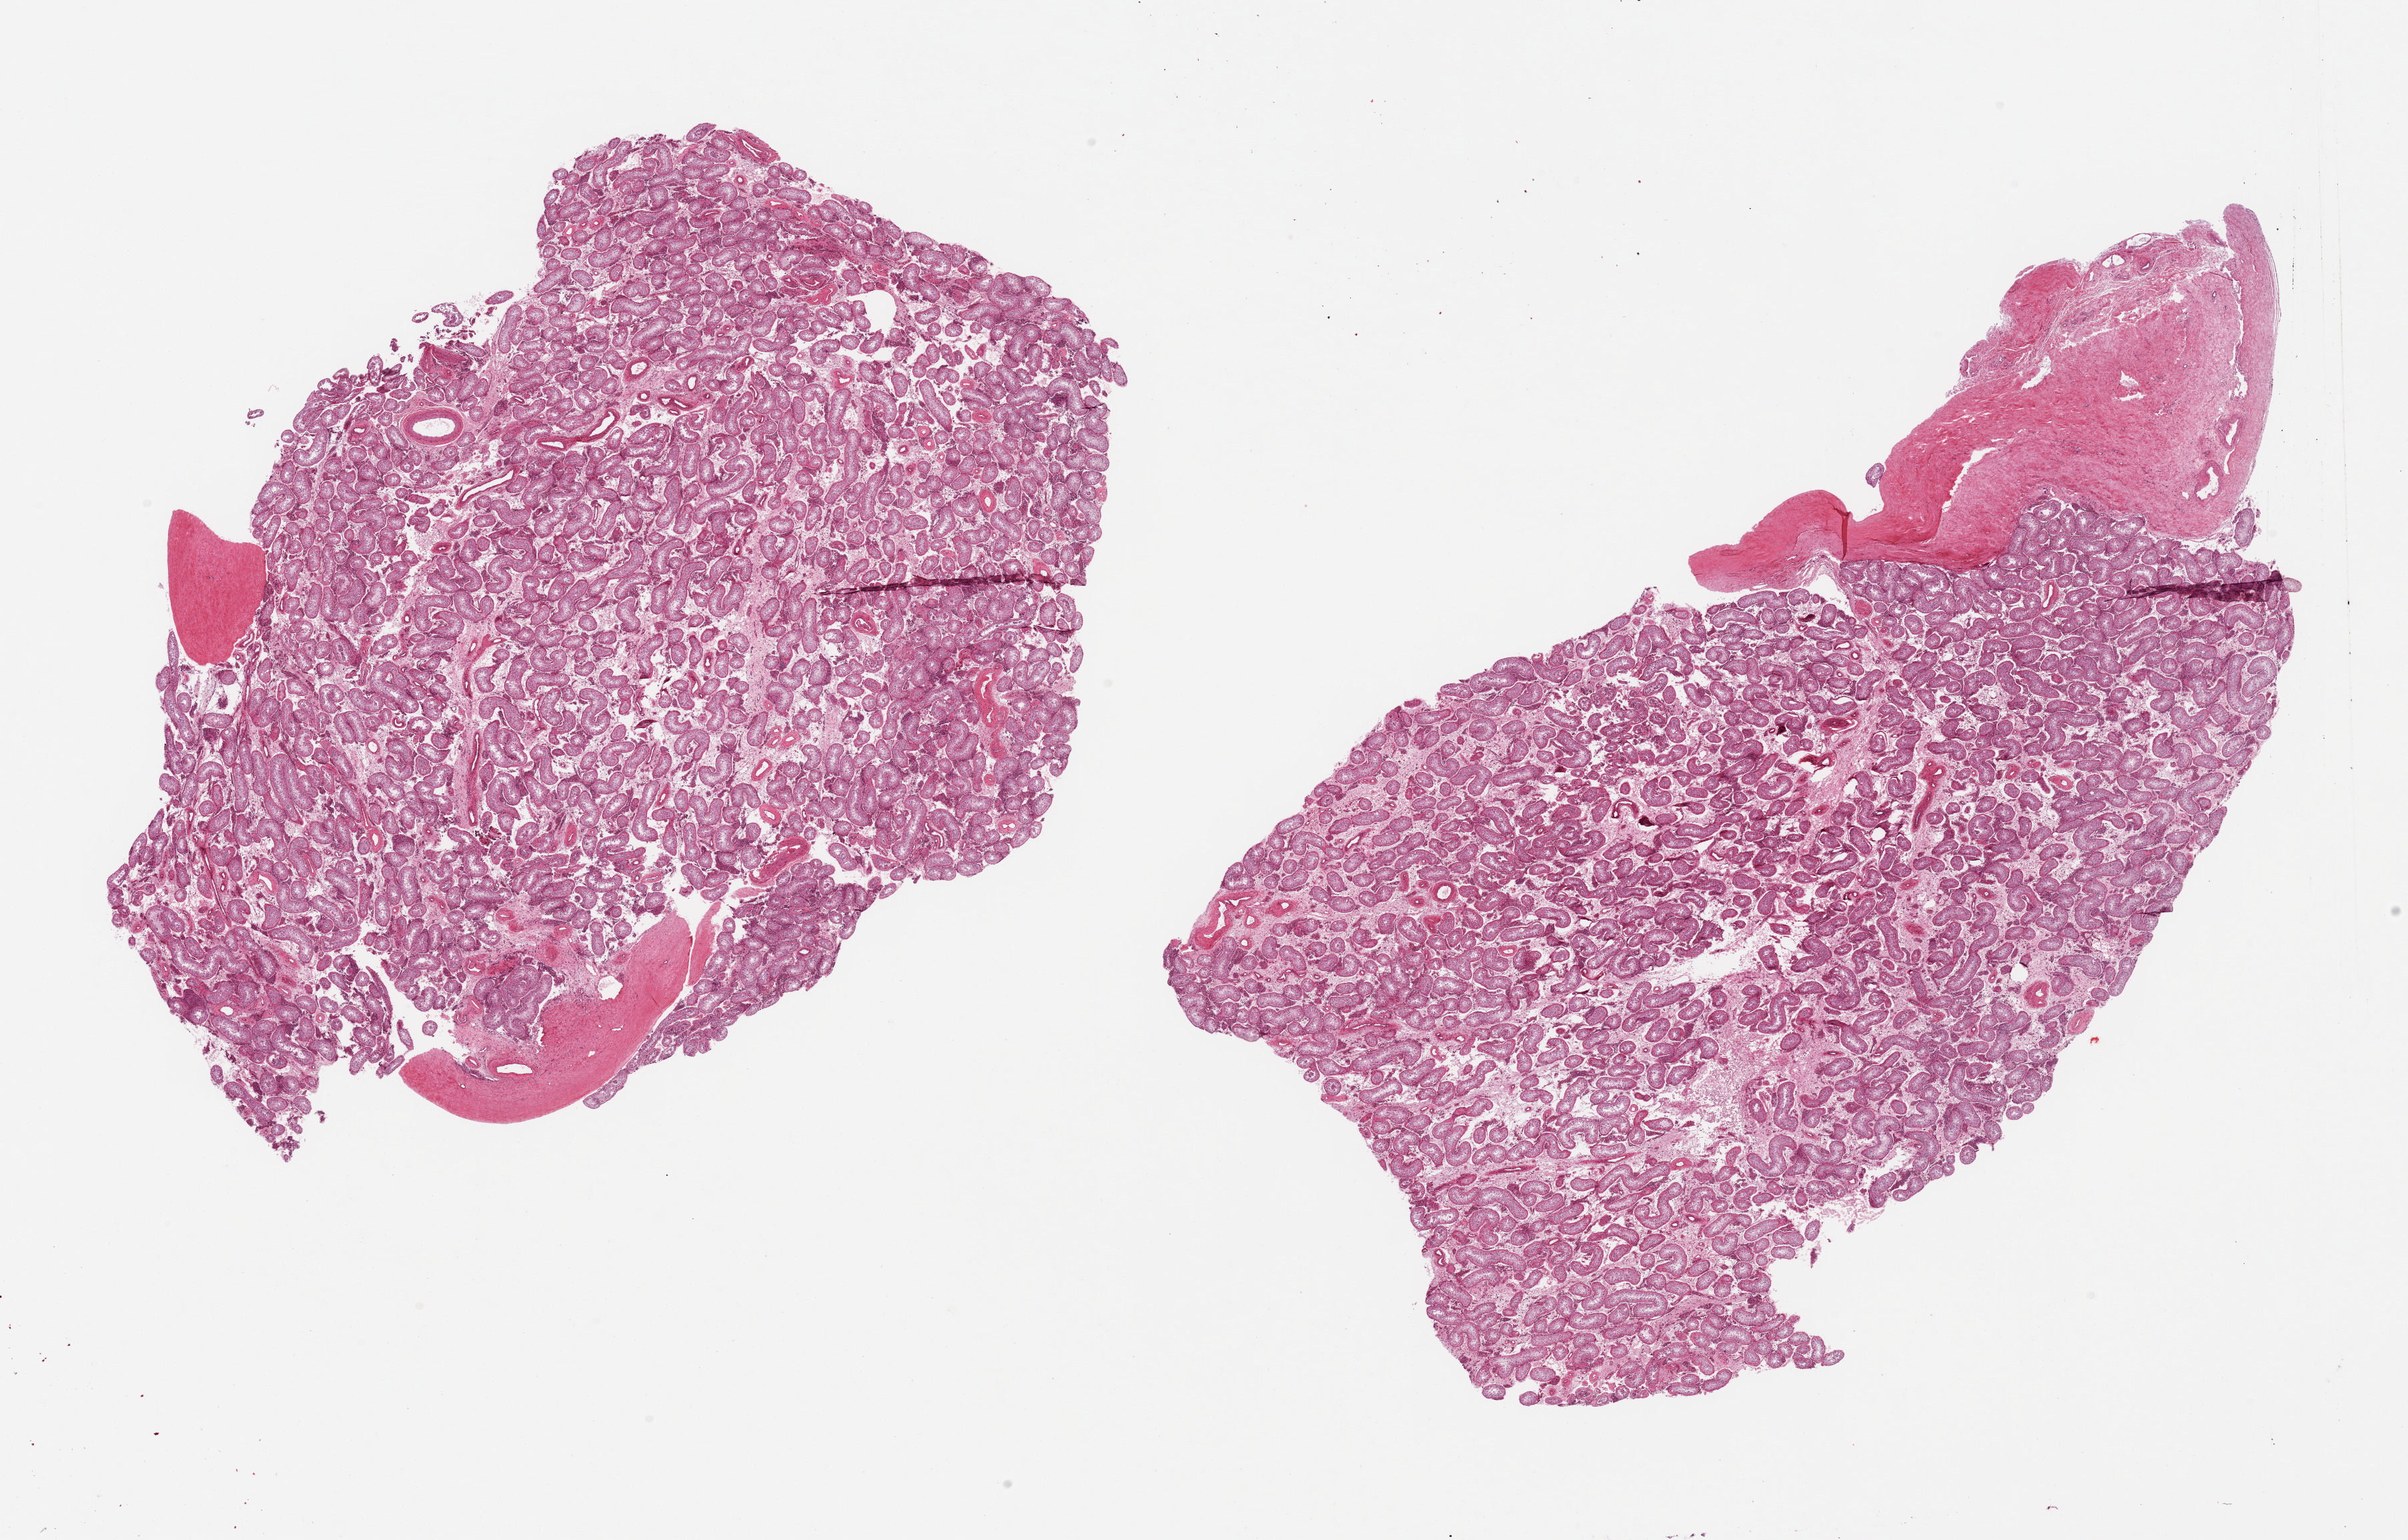
Digitized H&E-stained section, whole scanned area (about 28.5 x 18.3 mm, slide scanned at 20x) shown as a low-resolution overview; PAXgene-fixed paraffin-embedded (PFPE) section; section of testis (target tissue); tissue donor sample. Donor: male.
Reviewer comment on this tissue sample: 2 pieces 13x8 & 11x11 mm; complete arrest of spermatogenesis; only Sertoli cells remain (germ cell aplasia).